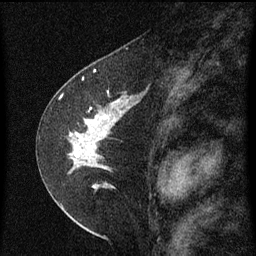
Breast MRI (dynamic contrast-enhanced), one sagittal slice; position 35 of 60 along the scan axis; dynamic contrast-enhanced series, image 2 of 3 at this slice position (ordered by acquisition); 1.5 T; TE 4.2 ms, TR 8 ms; 2 mm slice thickness; 256 × 256 image matrix, field of view 180 × 180 mm. Female patient, age 47 years.
Structures marked on this image (semi-automatic segmentation, software-assisted and operator-edited):
- analysis volume of interest (the breast-tissue region the enhancement analysis was run in; not a lesion): bounding box [x1, y1, x2, y2] px = [44, 84, 147, 199]
- tumour enhancement mask (voxels above the 70 % enhancement threshold inside the analysis volume of interest): [70, 100, 129, 189]